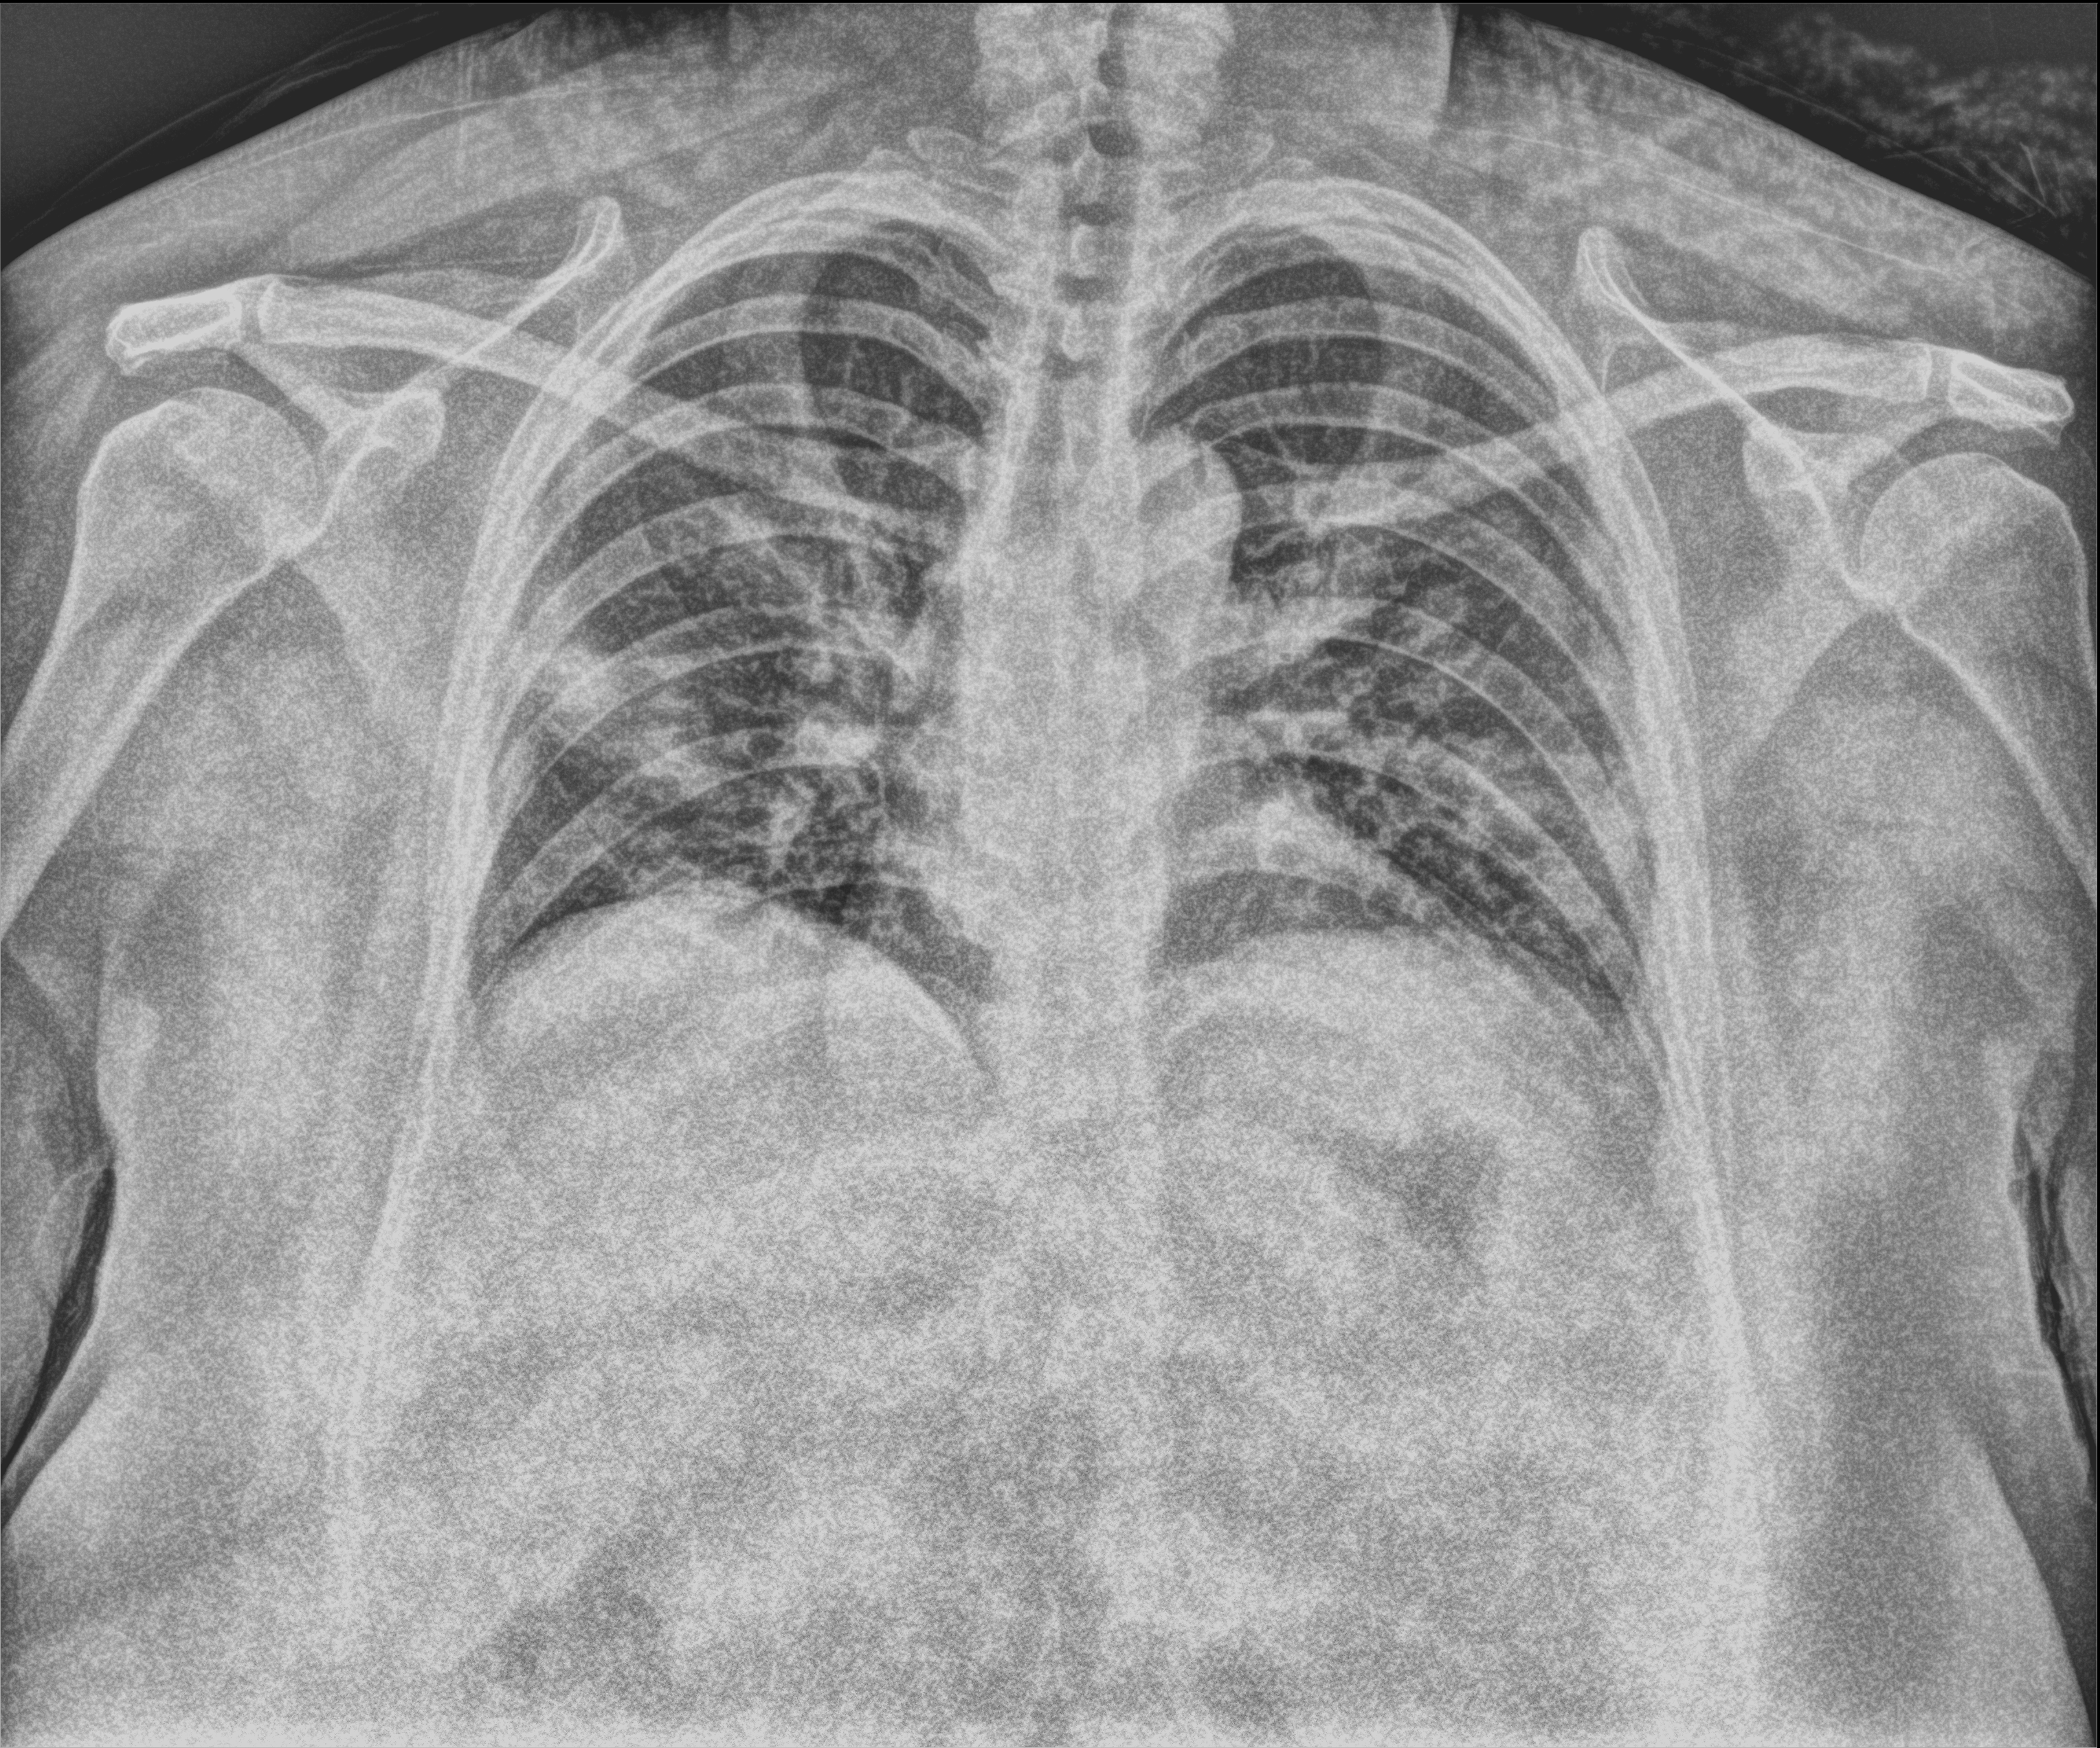
Bedside chest radiograph (computed radiography); anteroposterior (AP) projection. Female patient hospitalised with COVID-19, age 18–59 years.
From the hospital-stay record, not from the radiograph (when in the stay this image was taken is not recorded): length of hospital stay: 10 days; mechanically ventilated during this hospital stay: no; admitted to intensive care during this hospital stay: no.